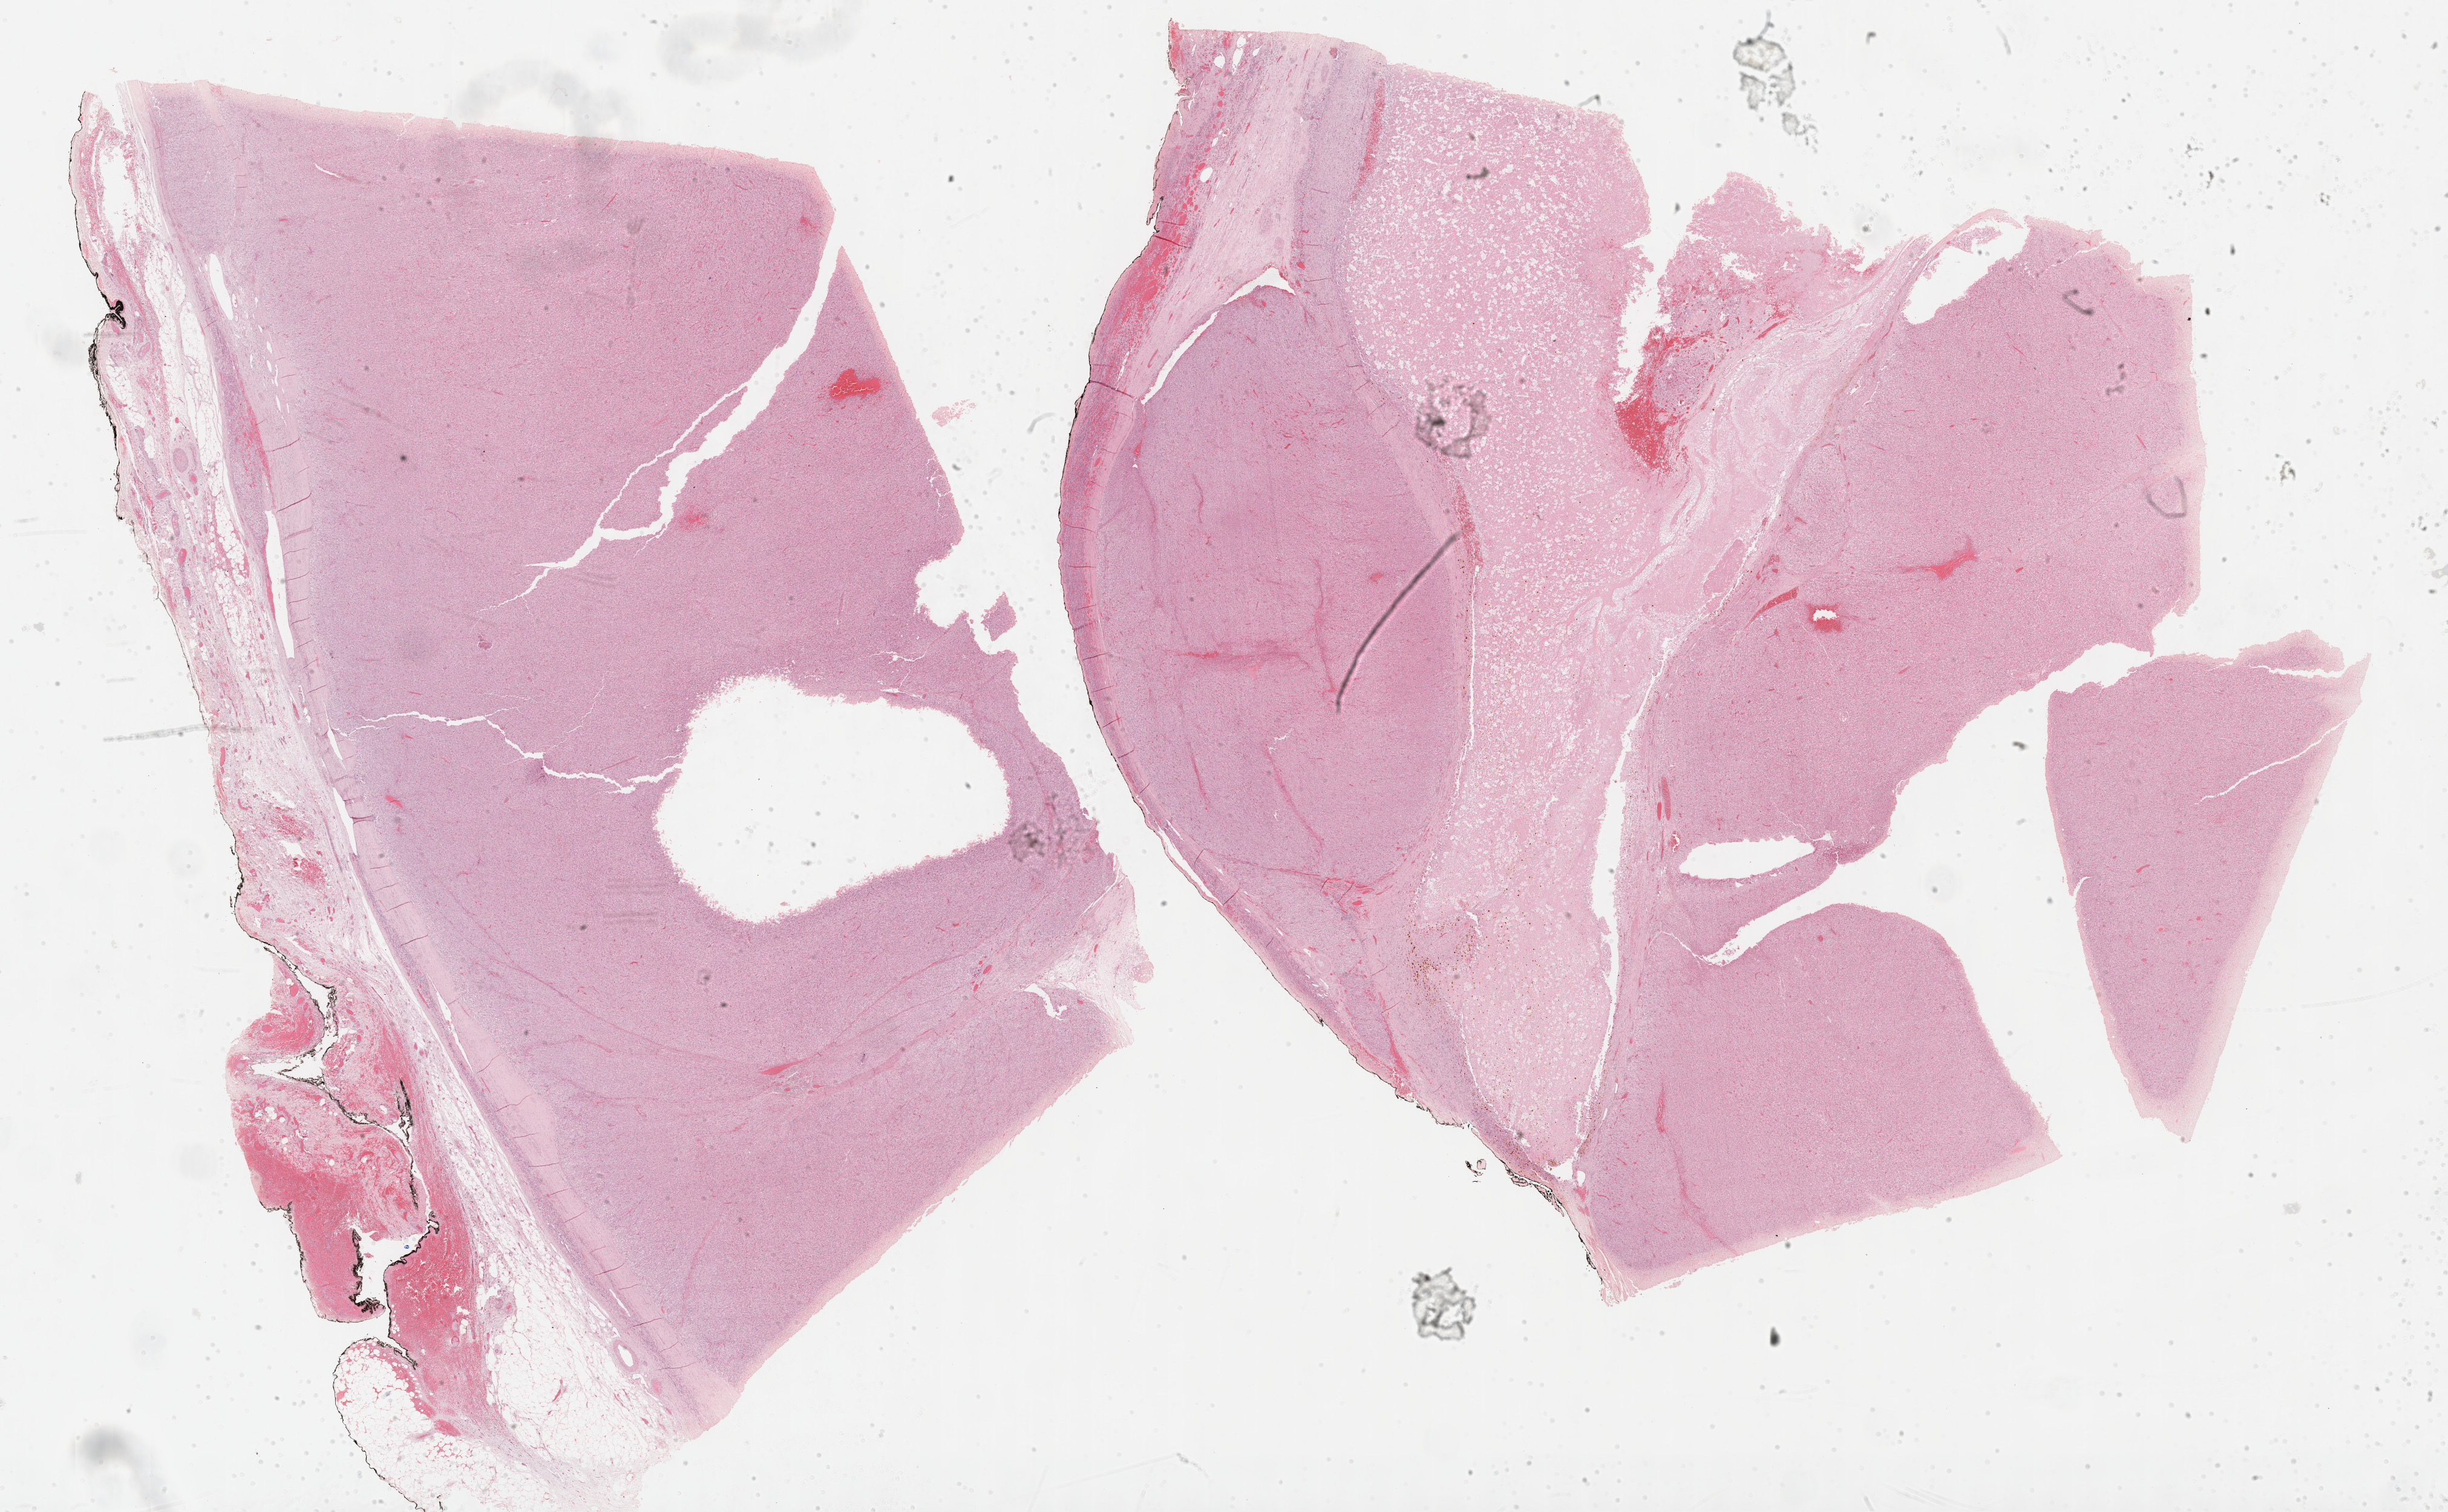
Whole-slide histology image, H&E-stained, whole scanned area (about 32.7 x 20.2 mm, slide scanned at 40x) shown as a low-resolution overview; FFPE section; sample: primary tumour, adrenal cortex. Patient: male, age at initial diagnosis 48 years.
Diagnosis: Adrenal cortical carcinoma (cortex of adrenal gland). Laterality: left.